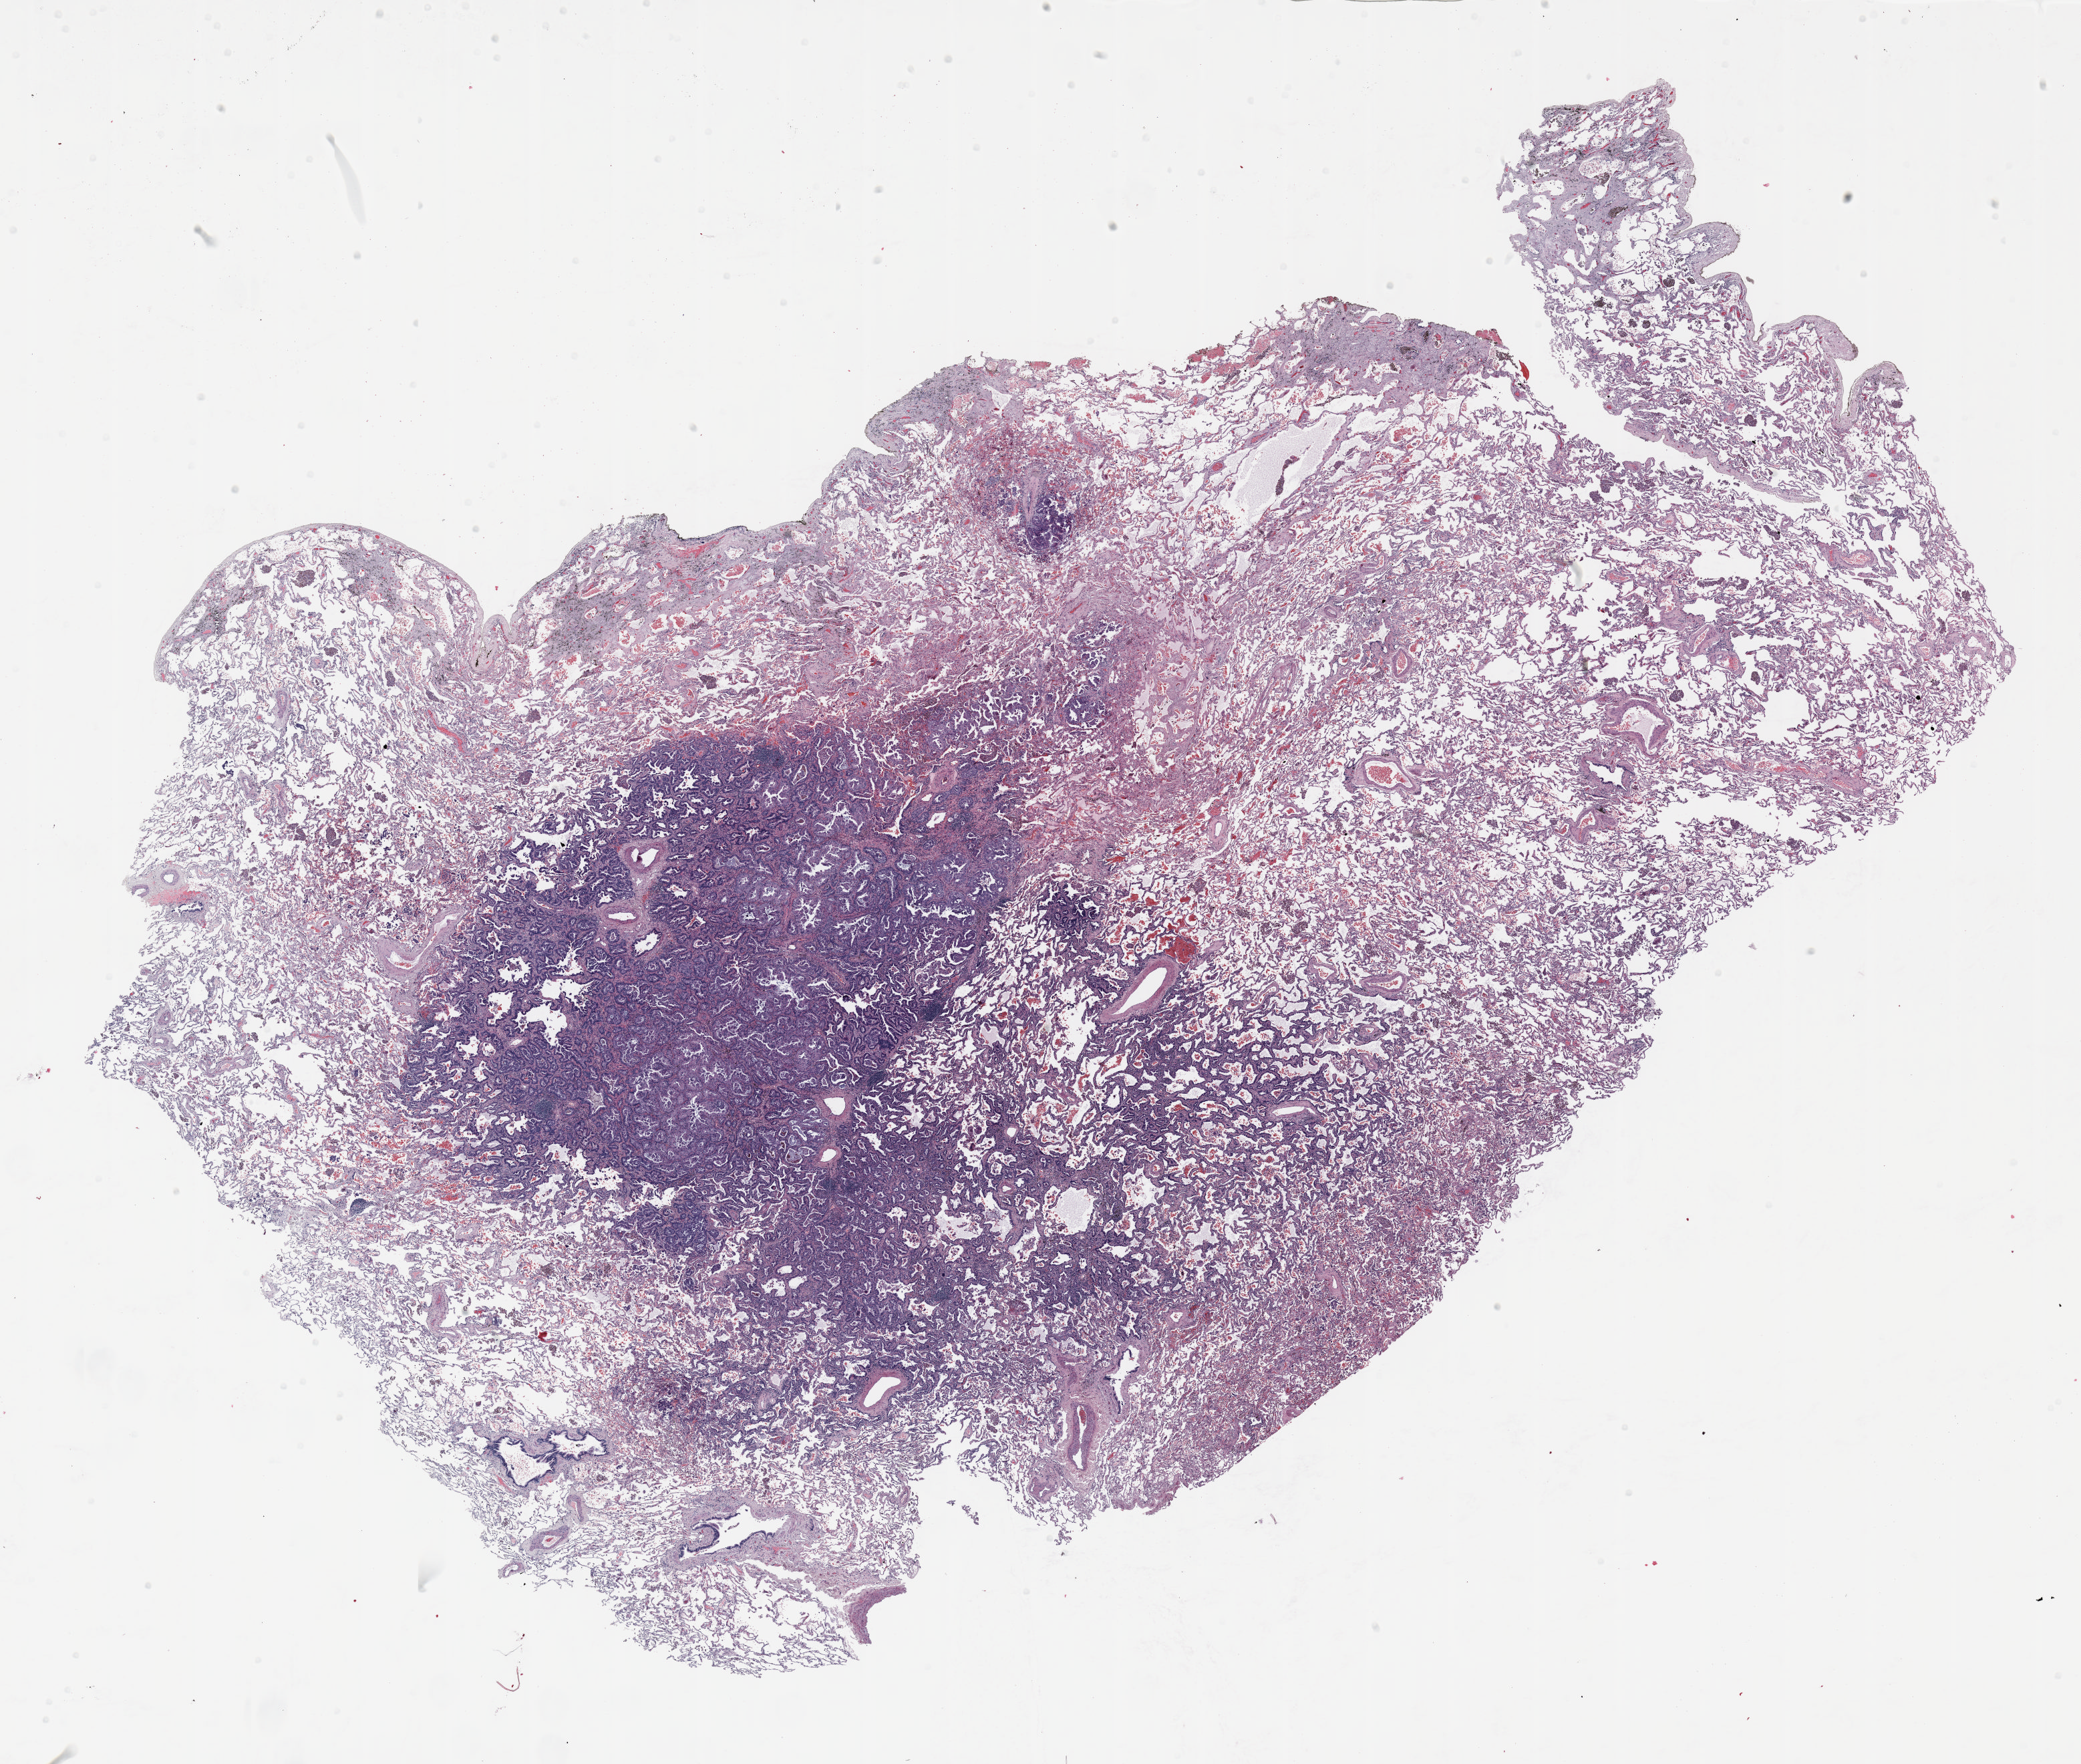
Whole-slide histology image, Hematoxylin and eosin (H&E) stained, a low-resolution overview of the entire scanned area, about 25.0 x 21.2 mm, FFPE section, lung tissue. Female, age 57 at enrolment. Current smoker at enrolment. Grade: moderately differentiated (G2).
- ICD-O-3 topography: upper lobe of lung (C34.1)
- tumour size (pathology): 15 mm
- participant's lung-cancer diagnosis: Adenocarcinoma, NOS (ICD-O-3 8140/3)
- stage (AJCC 6th edition): IA
- primary tumour location (clinical record): right upper lobe